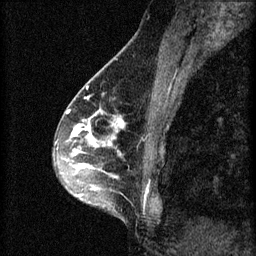
Breast MRI (dynamic contrast-enhanced), one sagittal slice; position 27 of 60 along the scan axis; 3 images stored at this slice position (order not interpretable as contrast timing); 1.5 T; TE 4.2 ms, TR 8.2 ms; 256 × 256 image matrix, field of view 180 × 180 mm. Patient: female, 45 years.
Structures marked on this image (semi-automatic segmentation, software-assisted and operator-edited):
- analysis volume of interest (the breast-tissue region the enhancement analysis was run in; not a lesion): bounding box [x1, y1, x2, y2] px = [54, 104, 159, 215]
- tumour enhancement mask (voxels above the 70 % enhancement threshold inside the analysis volume of interest): [62, 108, 125, 197]